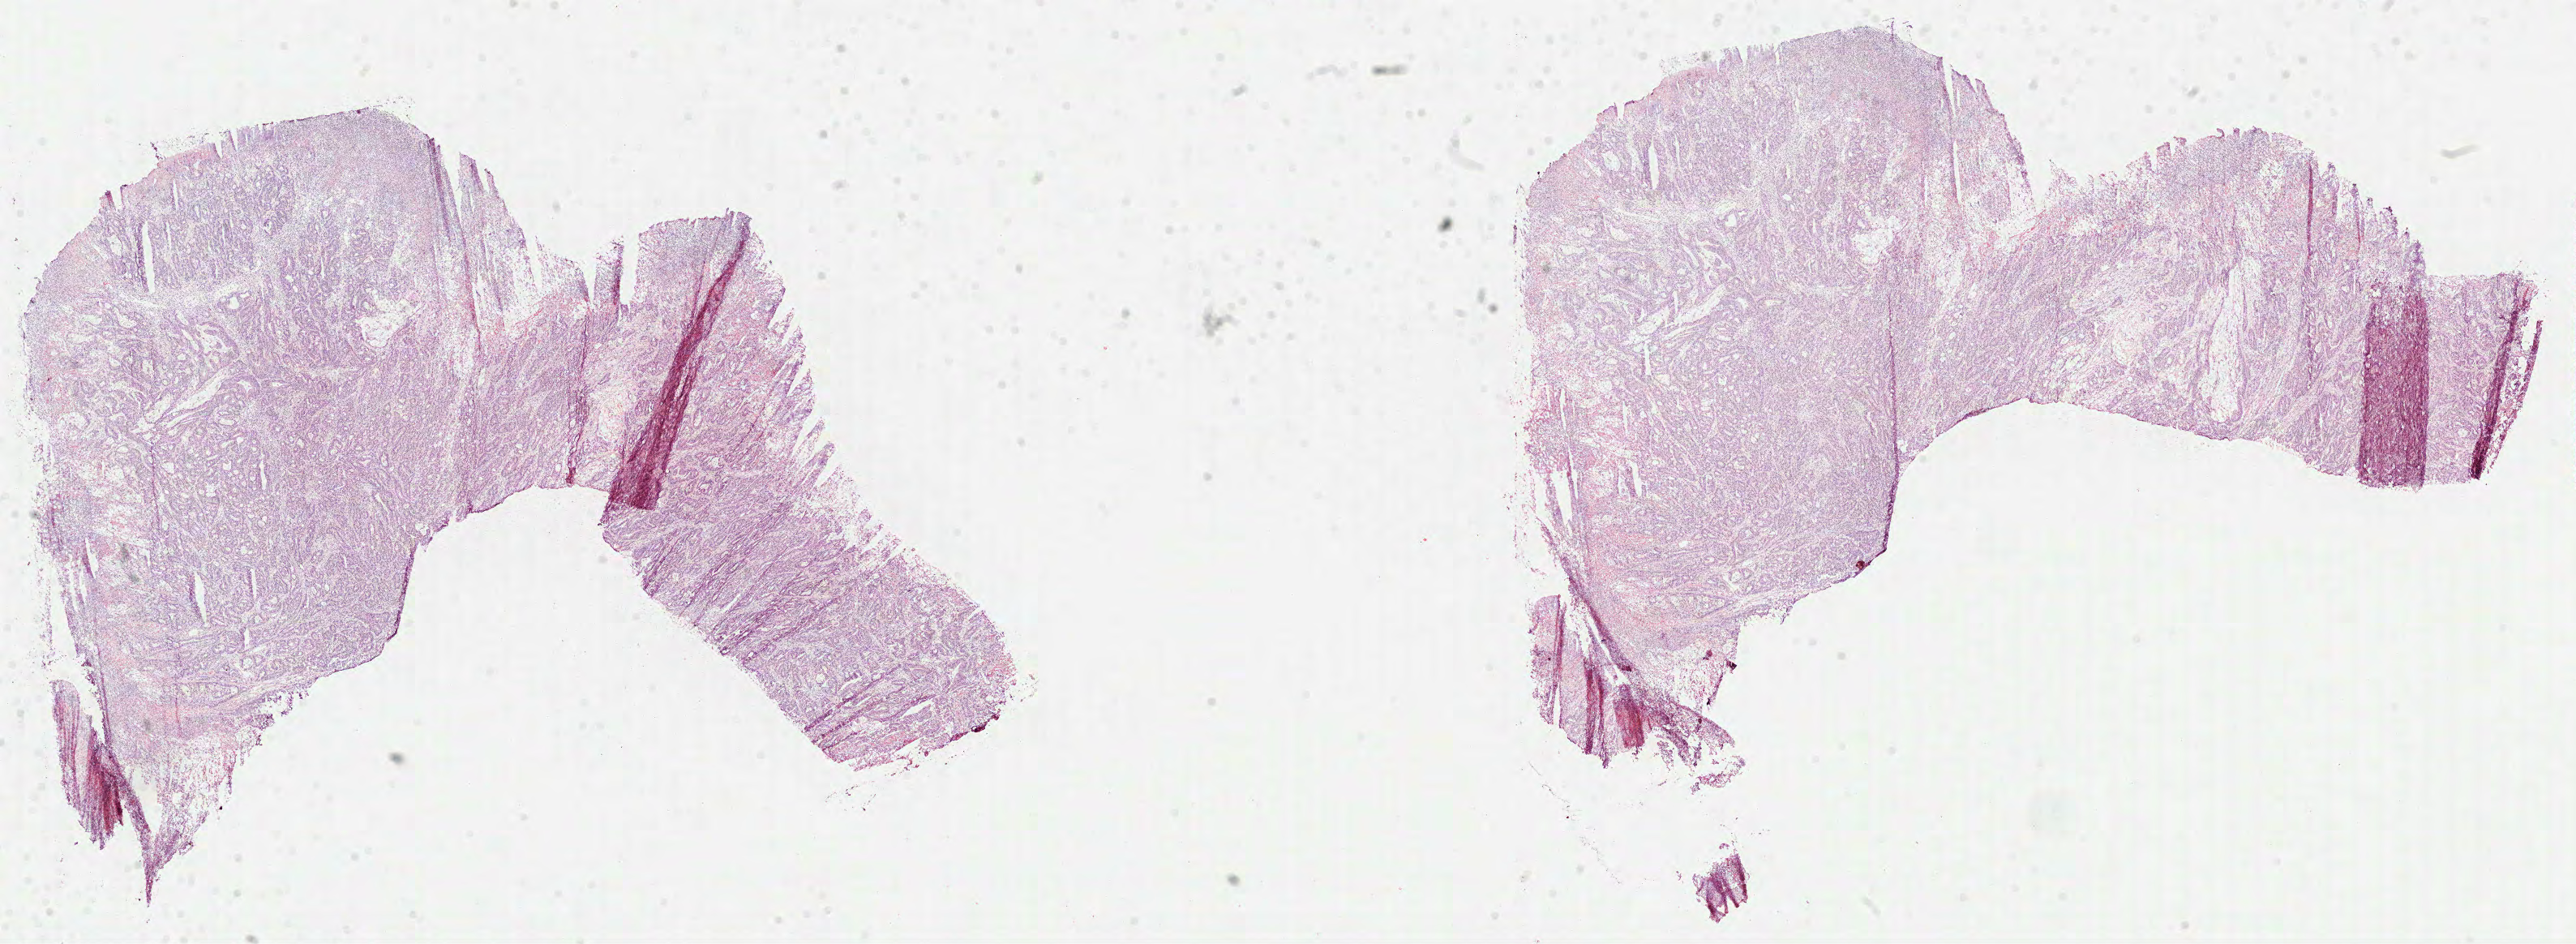
Whole-slide histology image, Hematoxylin and eosin (H&E) stained — low-resolution overview of the scanned area, about 25.6 x 9.4 mm, formalin-fixed paraffin-embedded (FFPE) diagnostic section, sample: primary tumour, colon. Male, age 34 years at initial diagnosis.
AJCC pathologic stage: IIA (7th edition). Diagnosis: Adenocarcinoma, NOS (sigmoid colon).